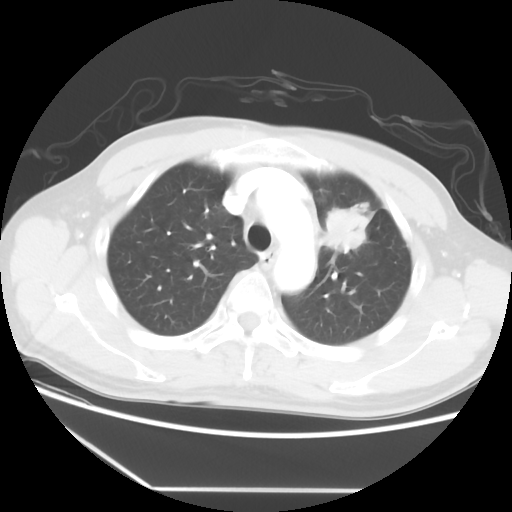
Chest CT, one axial slice. Position 41 of 56 along the scan axis. 120 kVp. Lung window (W 1500 / L -600 HU). 5 mm slice thickness. 512 × 512 image matrix, field of view 373 × 373 mm. Patient: male, 53 years. From the clinical record (not read from this slice): clinical TNM (as recorded): T2a N1 M1b.
Structures marked on this image (rectangle marked by the reading radiologist):
- lung tumour (recorded histology: adenocarcinoma): bounding box <318,203,369,254> (left, top, right, bottom; pixels)